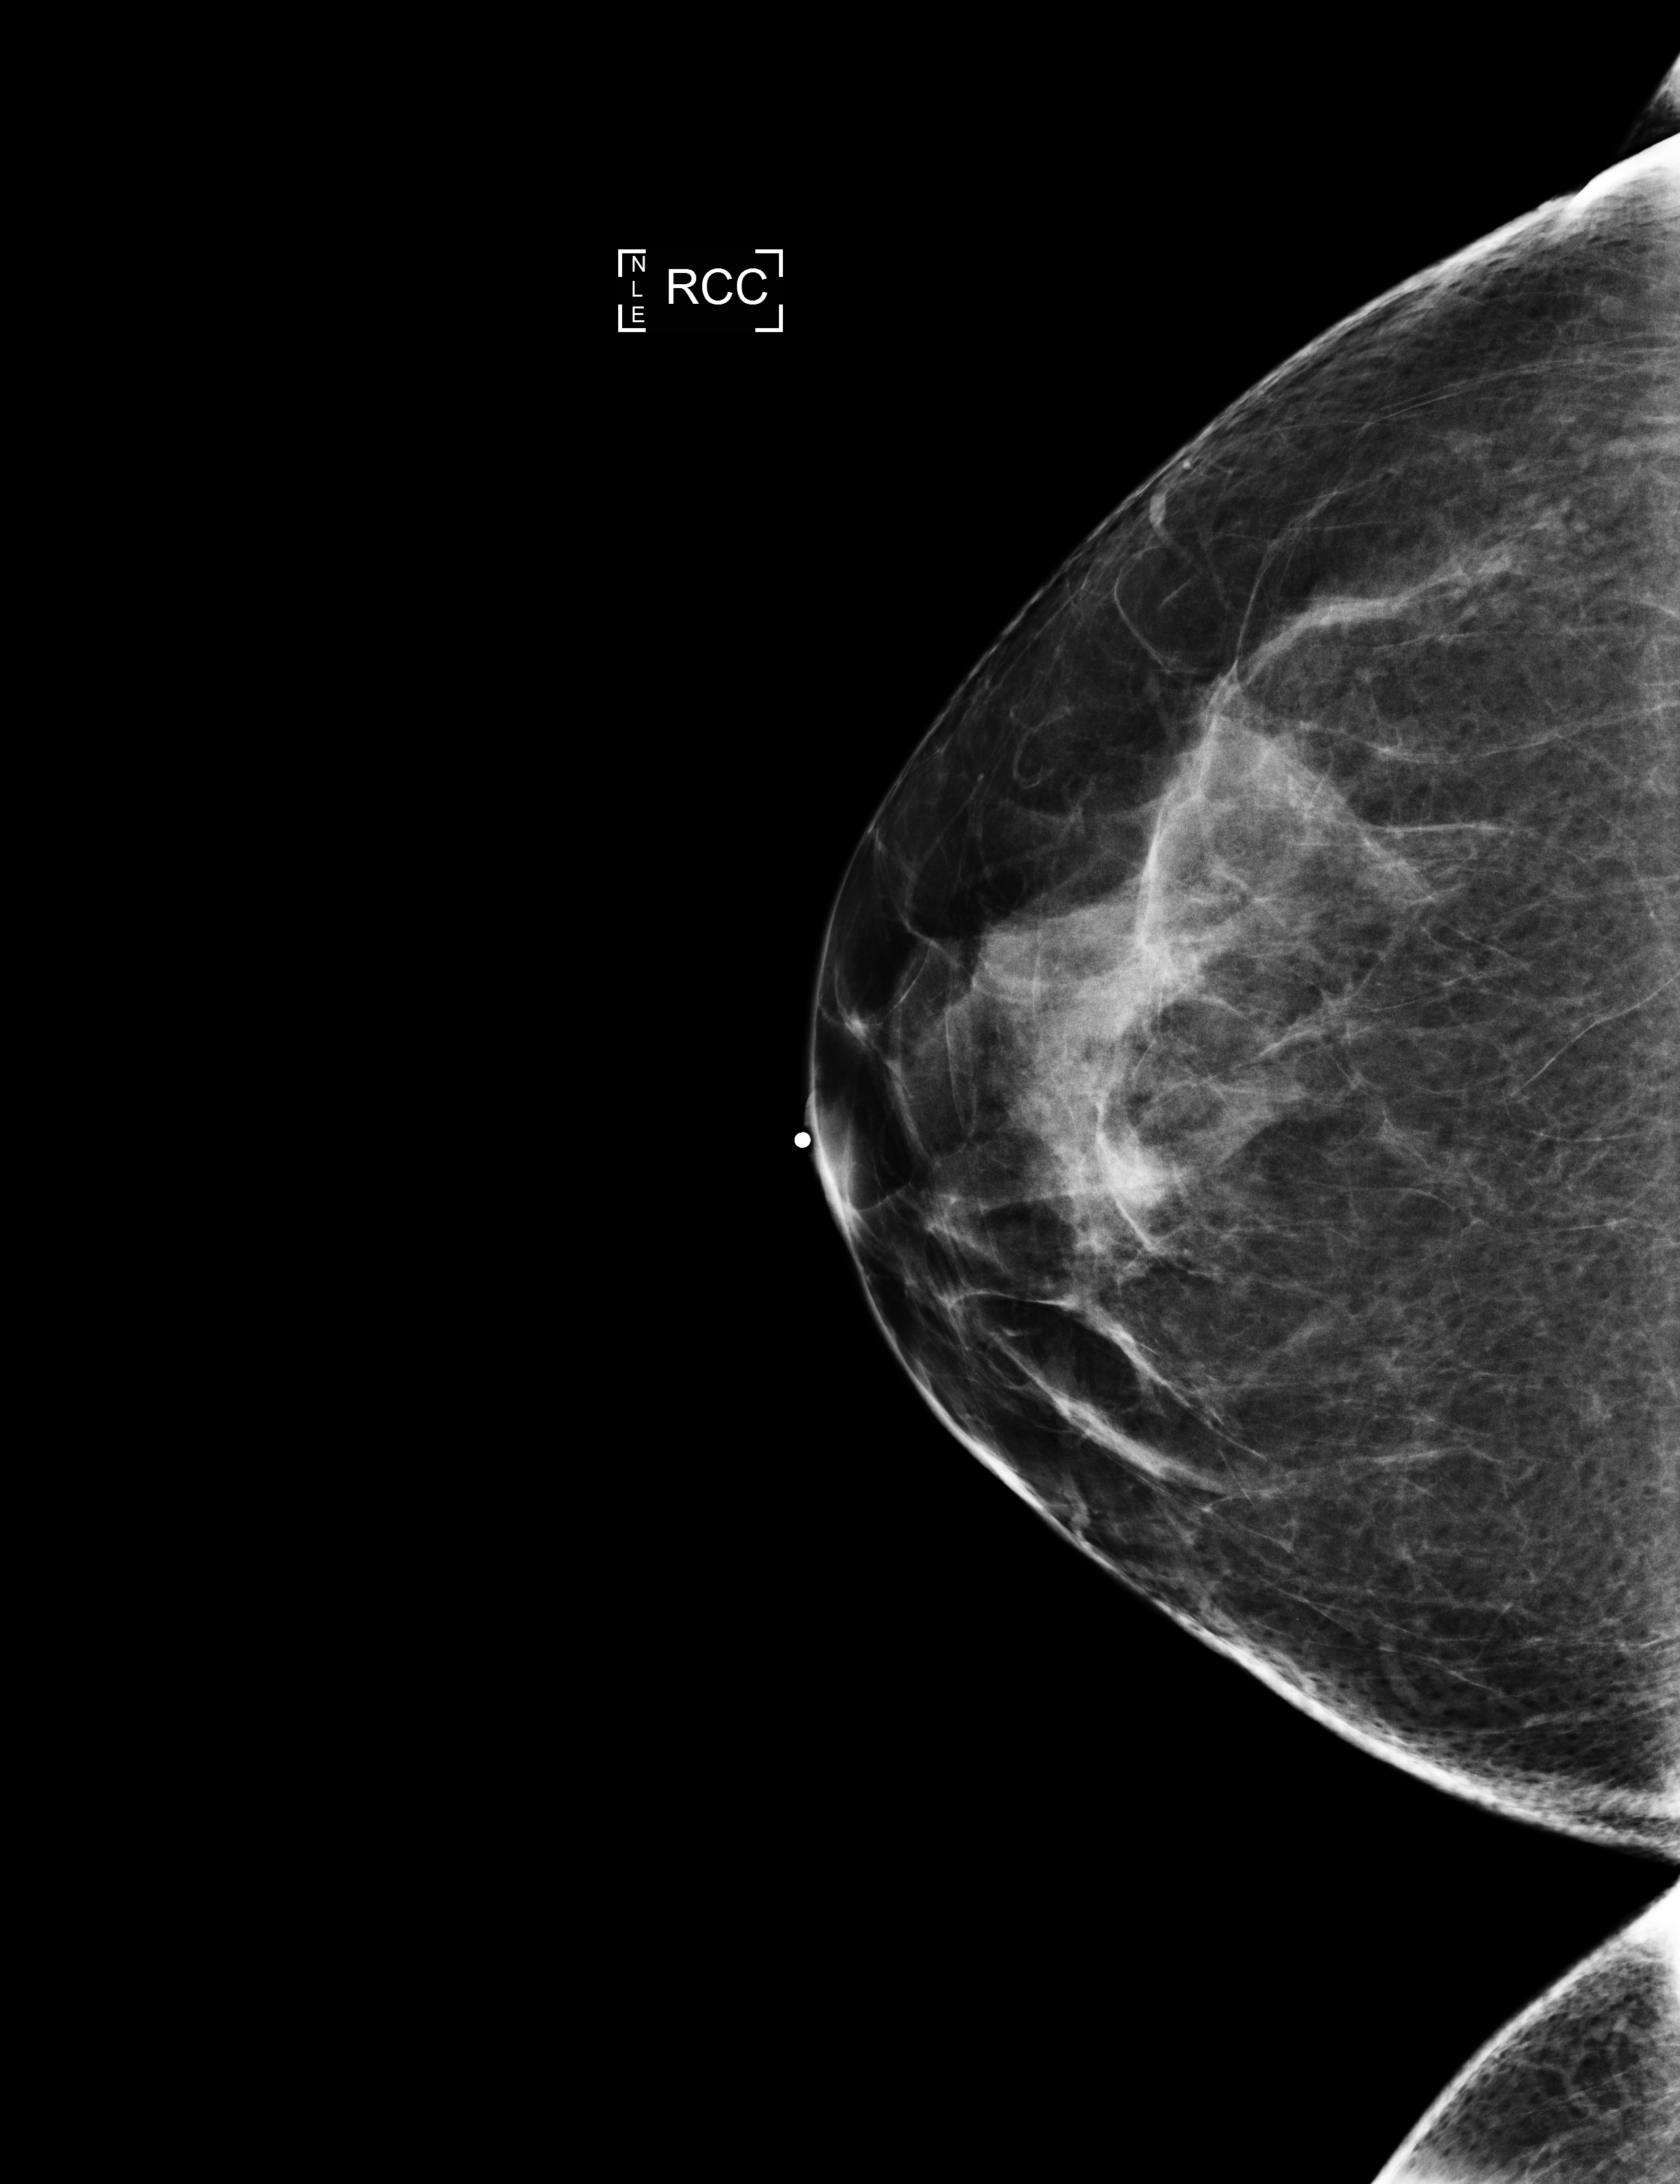
Annual screening mammography examination.
Image type: full-field digital mammogram. Breast: right. Projection: craniocaudal (CC) view.